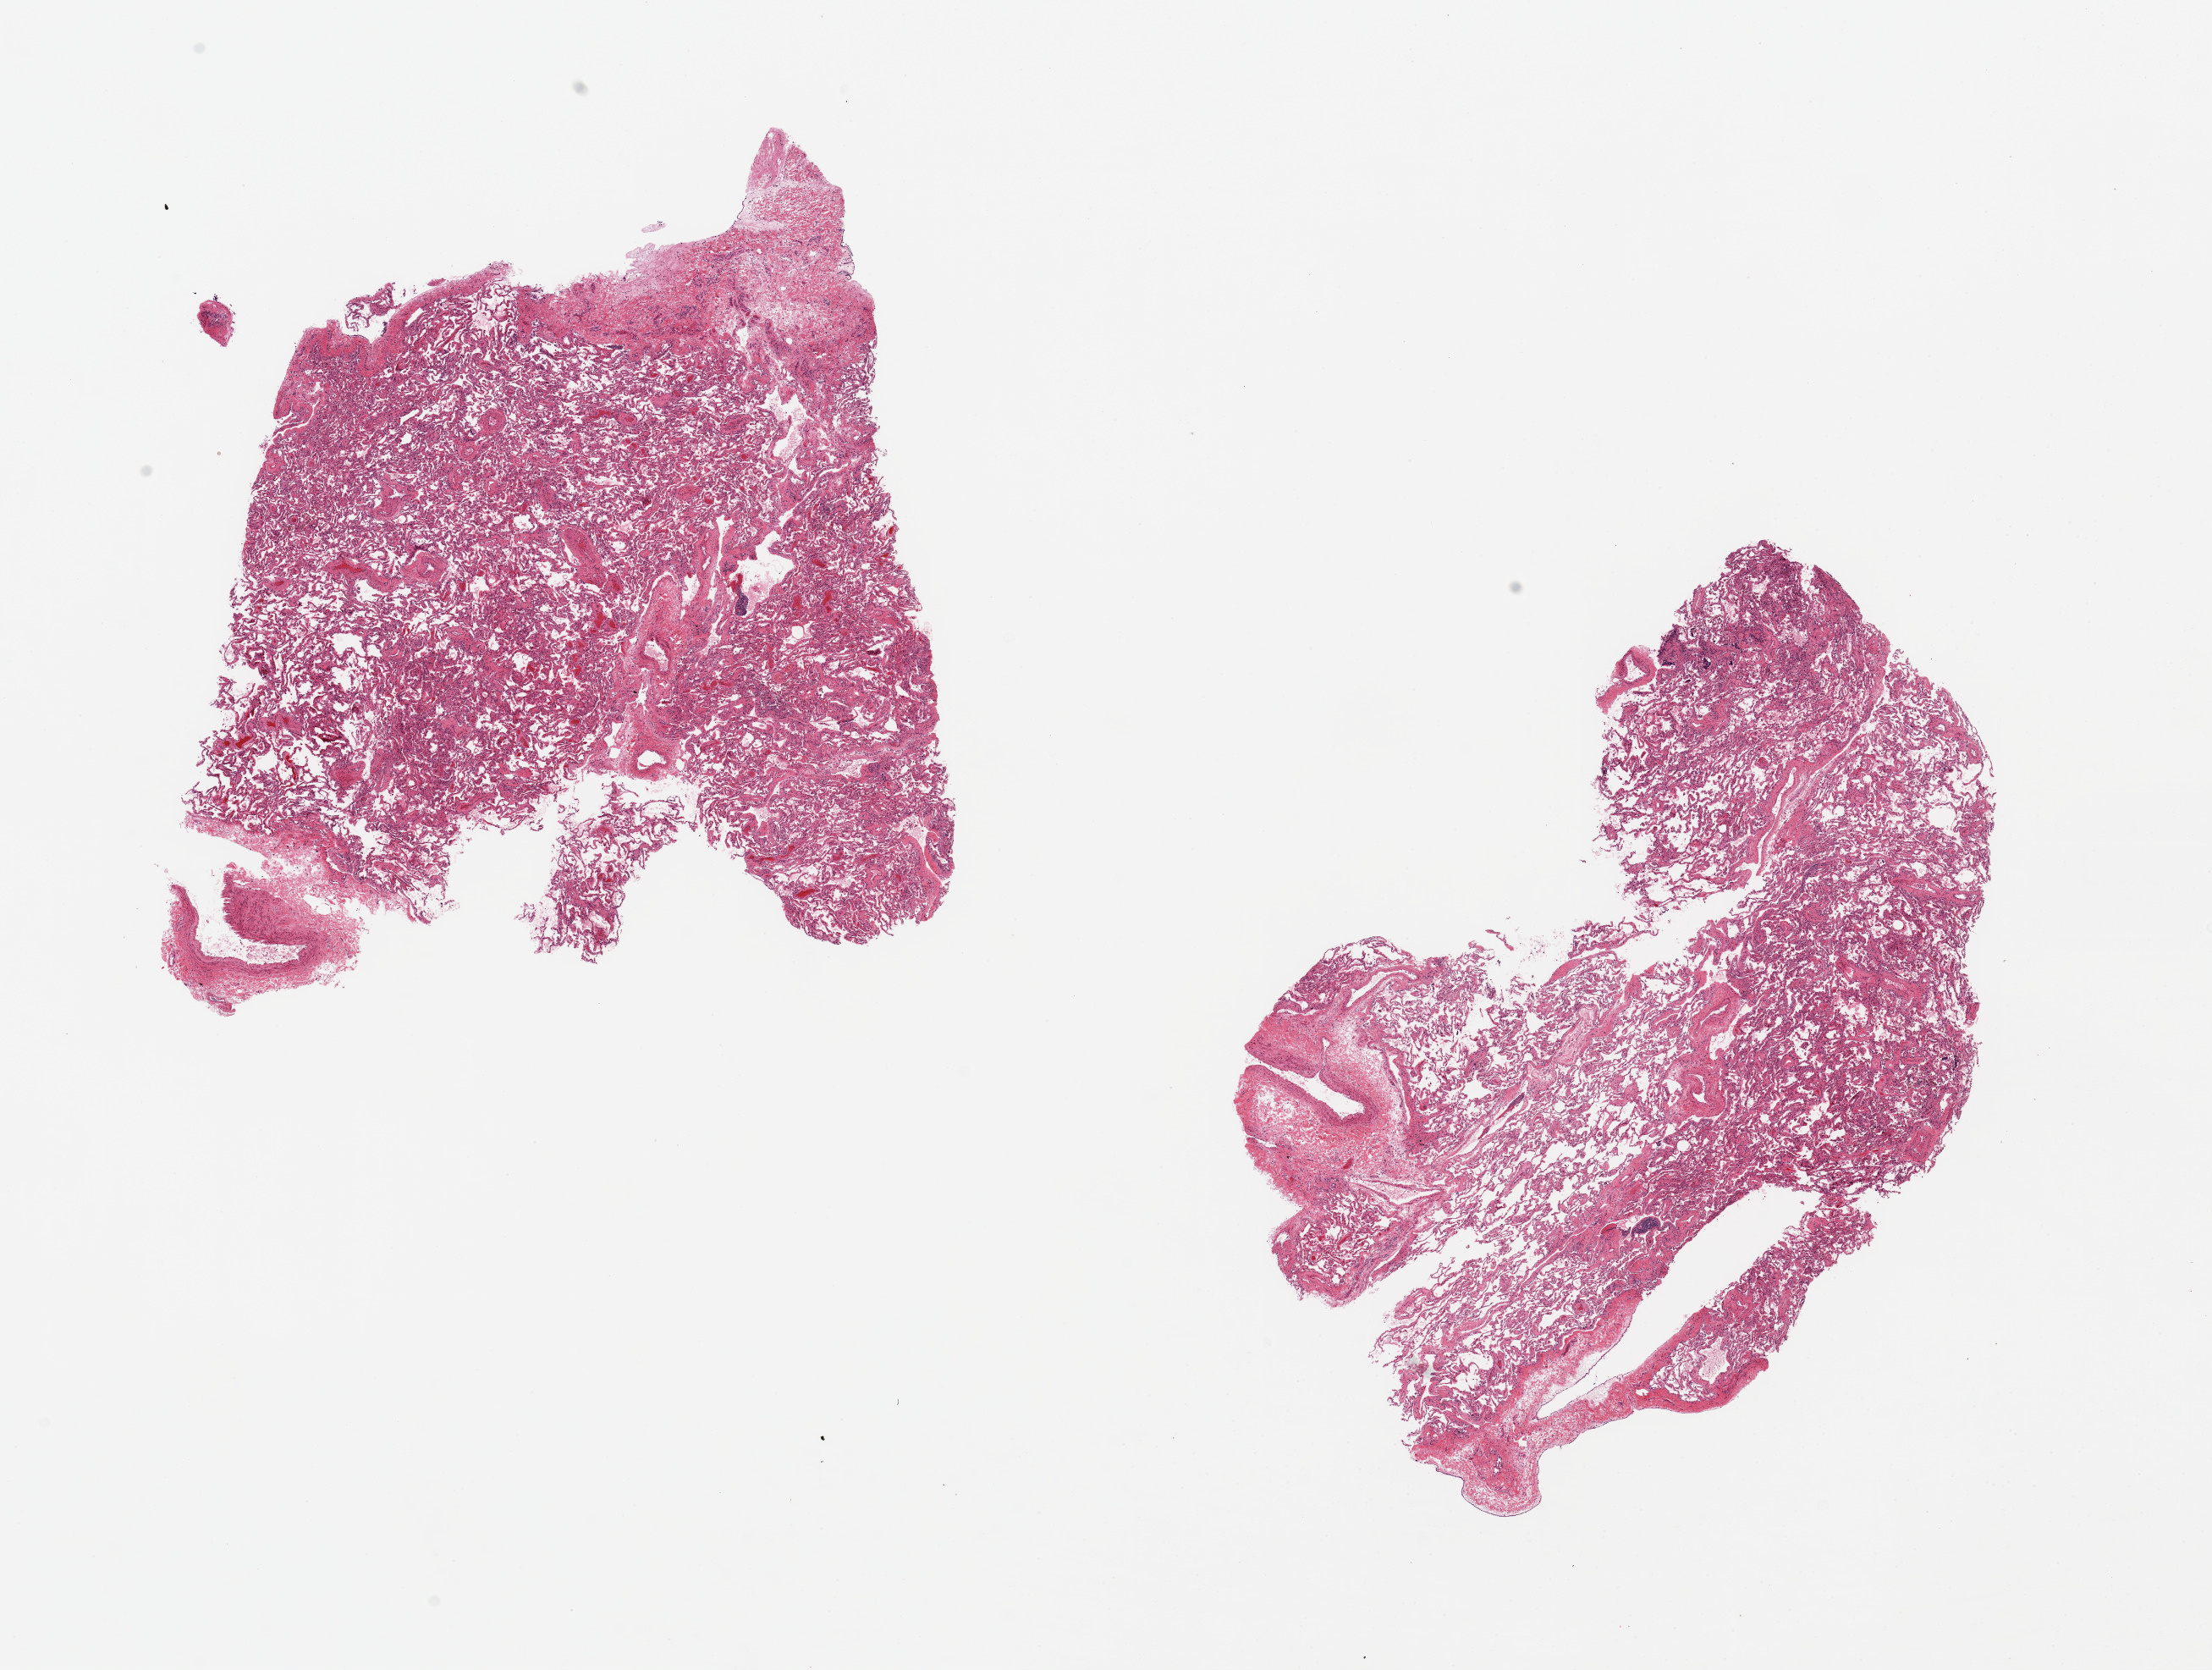
Digitized H&E-stained section, whole scanned area (about 20.7 x 15.6 mm, acquisition: 20x scan) shown as a low-resolution overview, PAXgene-fixed, paraffin-embedded tissue, section of lung (target tissue), tissue donor sample. Donor sex: male.
• pathologist's review note for this sample: 2 pieces; many pigmented macrophages, sections include some large vessels